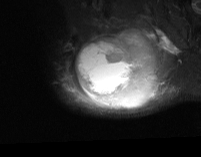
MRI of an extremity soft-tissue mass, one axial slice; slice 53 of 74 in the series (ordered by position); STIR; MR volume resampled by the dataset authors to the PET/CT grid (not the native acquisition matrix); 201 × 157 image matrix, field of view 196 × 153 mm. Male patient. Case-level facts recorded for this patient, not image findings: histological type: pleiomorphic spindle cell undifferentiated; grade: high; site of the primary tumour: right parascapusular.
Outlined on this slice (expert contour drawn on MRI and transferred to this co-registered scan by the dataset authors):
- gross tumour volume including surrounding oedema: box from (x=67, y=30) to (x=178, y=110) px
- gross tumour volume (mass): (x=76, y=36)–(x=155, y=108)